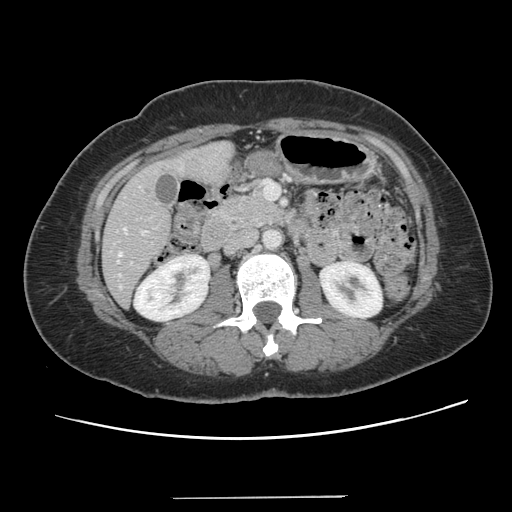
Contrast-enhanced abdominal CT, one axial slice. Slice 47 of 141 in the series (ordered by position). Intravenous contrast given. Soft-tissue window (W 400 / L 40 HU). 2.5 mm slice thickness. 512 × 512 image matrix, field of view 366 × 366 mm. Female patient, age 53 years. Case-level facts recorded for this patient, not image findings: diagnosis: colorectal cancer liver metastases, imaged before liver resection; multiple liver metastases: no; largest metastasis: 14.5 cm; disease in both lobes: yes.
Outlined on this slice (outlined manually by an expert reader):
- hepatic veins: bounding box <118,228,125,256> (left, top, right, bottom; pixels)
- liver: <103,144,231,305>
- planned liver remnant (the part of the liver to remain after resection): <103,218,171,305>